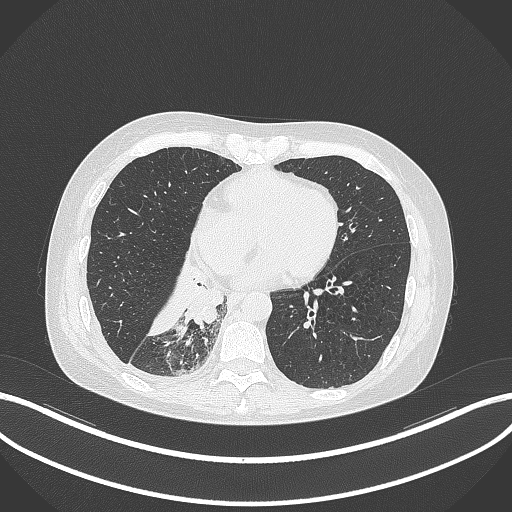
Chest CT, one axial slice; position 110 of 329 along the scan axis; reconstruction kernel B70f; 120 kVp; lung window (W 1500 / L -600 HU); 1 mm slice thickness; 512 × 512 image matrix, field of view 400 × 400 mm. Female patient, age 63 years. From the clinical record (not read from this slice): clinical TNM (as recorded): T1c N0 M0.
Structures marked on this image (rectangle marked by the reading radiologist):
- lung tumour (recorded histology: adenocarcinoma): bounding box [x1, y1, x2, y2] px = [180, 284, 226, 331]